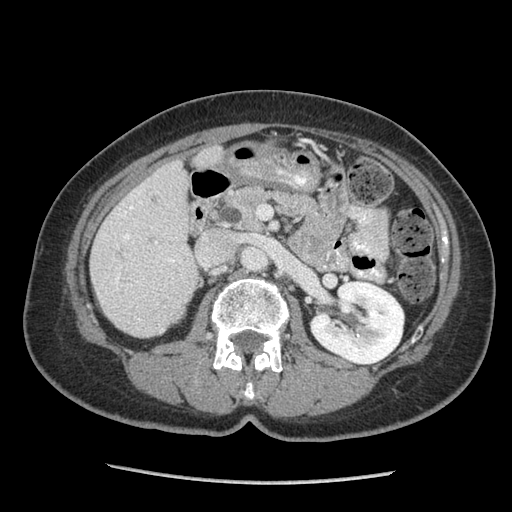
Contrast-enhanced abdominal CT (liver protocol), one axial slice. Slice 33 of 105 in the series (ordered by position). 140 kVp. Soft-tissue window (W 400 / L 40 HU). 512 × 512 image matrix. From the clinical record (not read from this slice): diagnosis: hepatocellular carcinoma (patient treated with transarterial chemoembolisation; whether this scan precedes or follows treatment is not stated here); TNM stage (as recorded): Stage-I; Child-Pugh class: A.
Annotated regions visible in this slice (semi-automatic segmentation, software-assisted and operator-edited):
- liver parenchyma outside the tumour (the mass and vessels are separate outlines, so this box may not span the whole liver): bounding box [x1, y1, x2, y2] px = [90, 146, 222, 336]
- liver vessels: [115, 191, 181, 321]